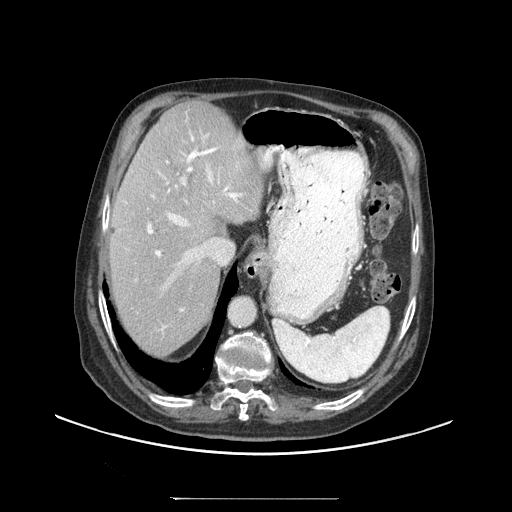
Contrast-enhanced abdominal CT (liver protocol), one axial slice. Position 73 of 97 along the scan axis. Reconstruction kernel STANDARD. Soft-tissue window (W 400 / L 40 HU). 512 × 512 image matrix, field of view 450 × 450 mm. Case-level facts recorded for this patient, not image findings: diagnosis: hepatocellular carcinoma (patient treated with transarterial chemoembolisation; whether this scan precedes or follows treatment is not stated here); TNM stage (as recorded): Stage-IIIC; Child-Pugh class: A.
Annotated regions visible in this slice (semi-automatically segmented with operator editing):
- abdominal aorta: box from (x=229, y=298) to (x=255, y=326) px
- liver parenchyma outside the tumour (the mass and vessels are separate outlines, so this box may not span the whole liver): (x=108, y=100)–(x=262, y=354)
- liver vessels: (x=125, y=134)–(x=242, y=331)